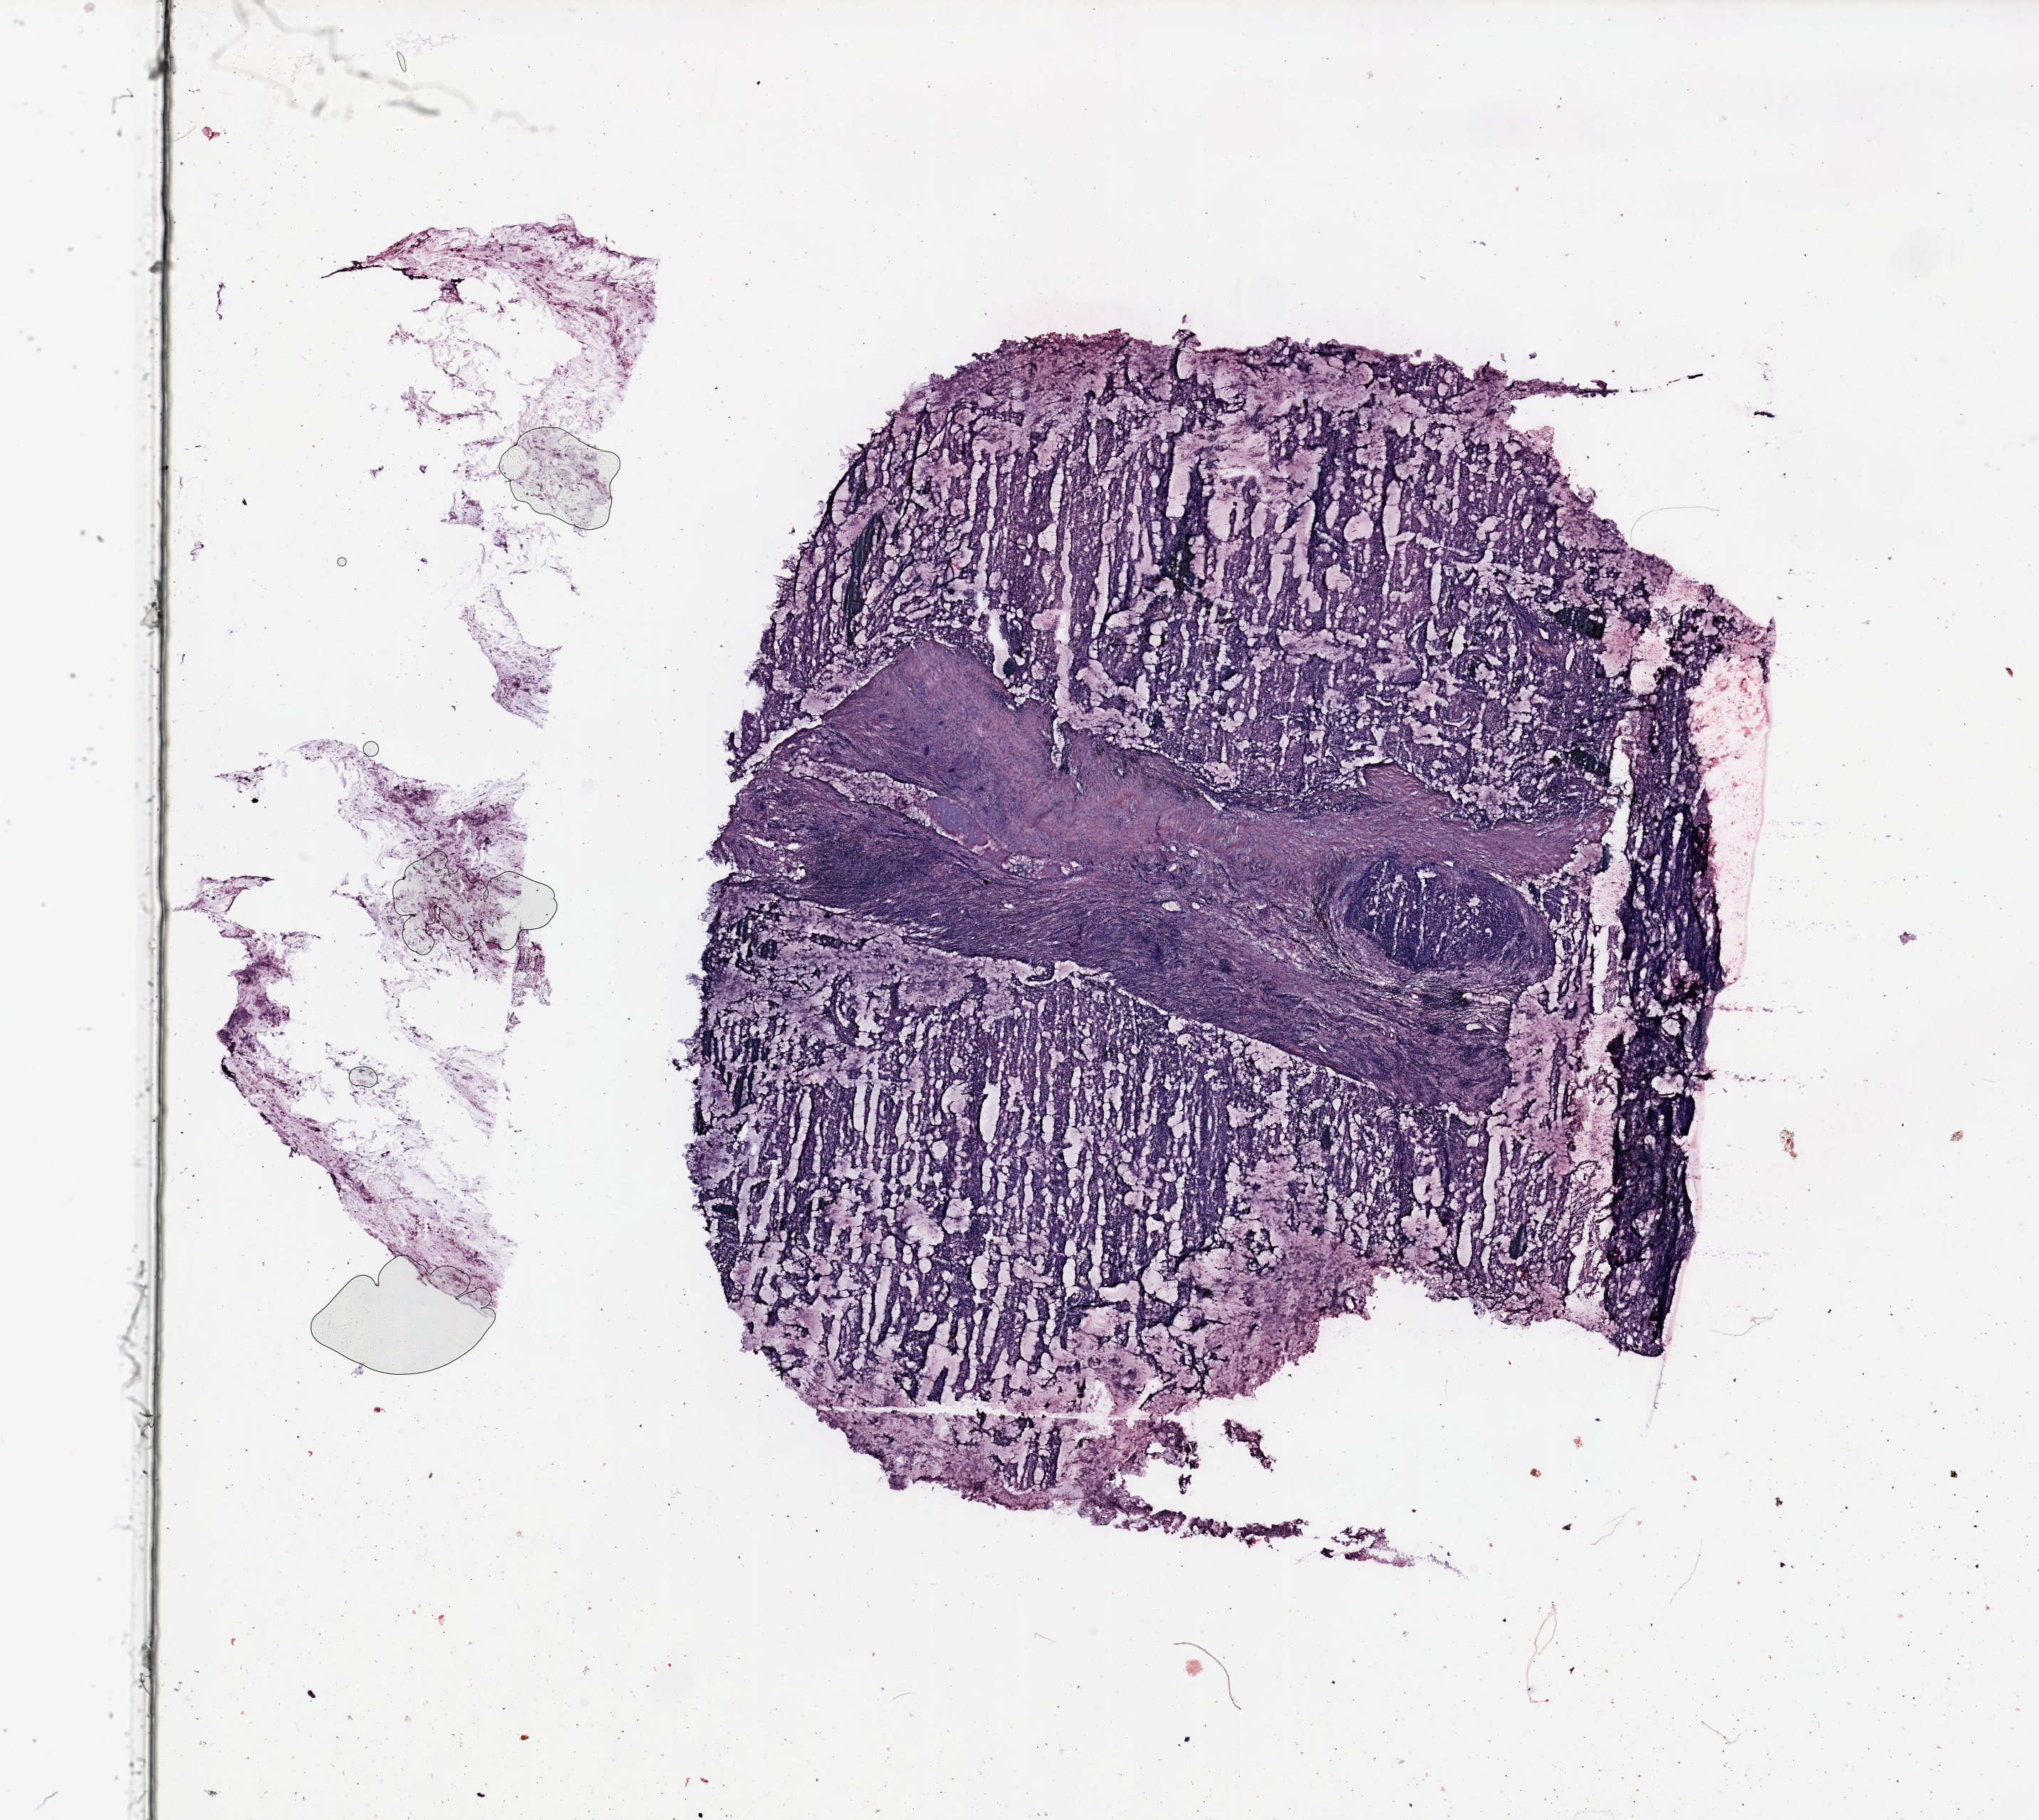
Digitized Hematoxylin and eosin (H&E) stained tissue section (whole slide) — whole scanned area (about 22.6 x 20.2 mm, from a 20x scan) shown as a low-resolution overview, kidney, tumour tissue. Patient: female, age 57 years. Histologic grade: G2 (moderately differentiated).
* histologic diagnosis: Renal cell carcinoma, NOS
* primary tumour site (as recorded): upper pole
* AJCC pathologic stage: I